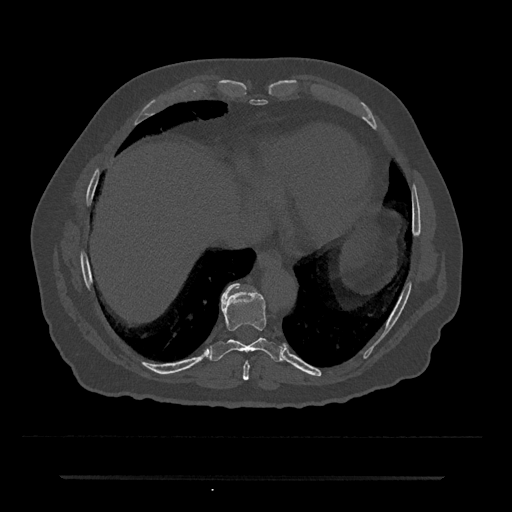
CT including the spine, one axial slice. Position 281 of 797 along the scan axis. Reconstruction kernel Br40s/3. 120 kVp. Bone window (W 1800 / L 400 HU). 0.5 mm slice thickness. 512 × 512 image matrix. Male patient, age 69 years. Case-level facts recorded for this patient, not image findings: primary cancer: prostate.
Outlined on this slice (semi-automatically segmented with operator editing):
- T8 vertebra: bounding box [x1, y1, x2, y2] px = [243, 361, 249, 380]
- T9 vertebra: [211, 283, 283, 362]